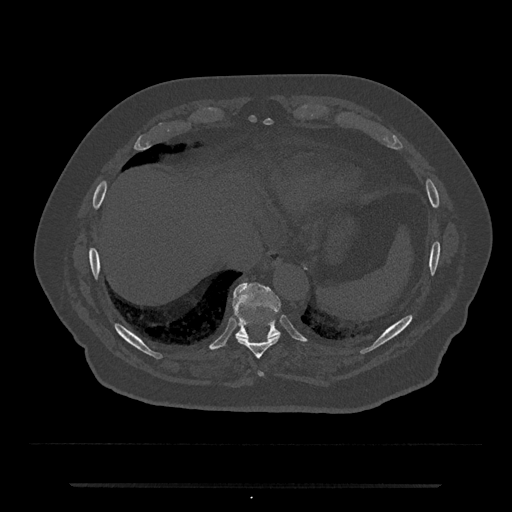
CT including the spine, one axial slice. Position 738 of 797 along the scan axis. 120 kVp. Bone window (W 1800 / L 400 HU). 0.5 mm slice thickness. 512 × 512 image matrix. Patient: male, 80 years. Case-level facts recorded for this patient, not image findings: primary cancer: prostate.
Annotated regions visible in this slice (semi-automatically segmented with operator editing):
- T10 vertebra: bounding box (x1, y1, x2, y2) in pixels: (233, 283, 280, 338)
- T8 vertebra: (258, 371, 263, 376)
- T9 vertebra: (236, 335, 280, 359)